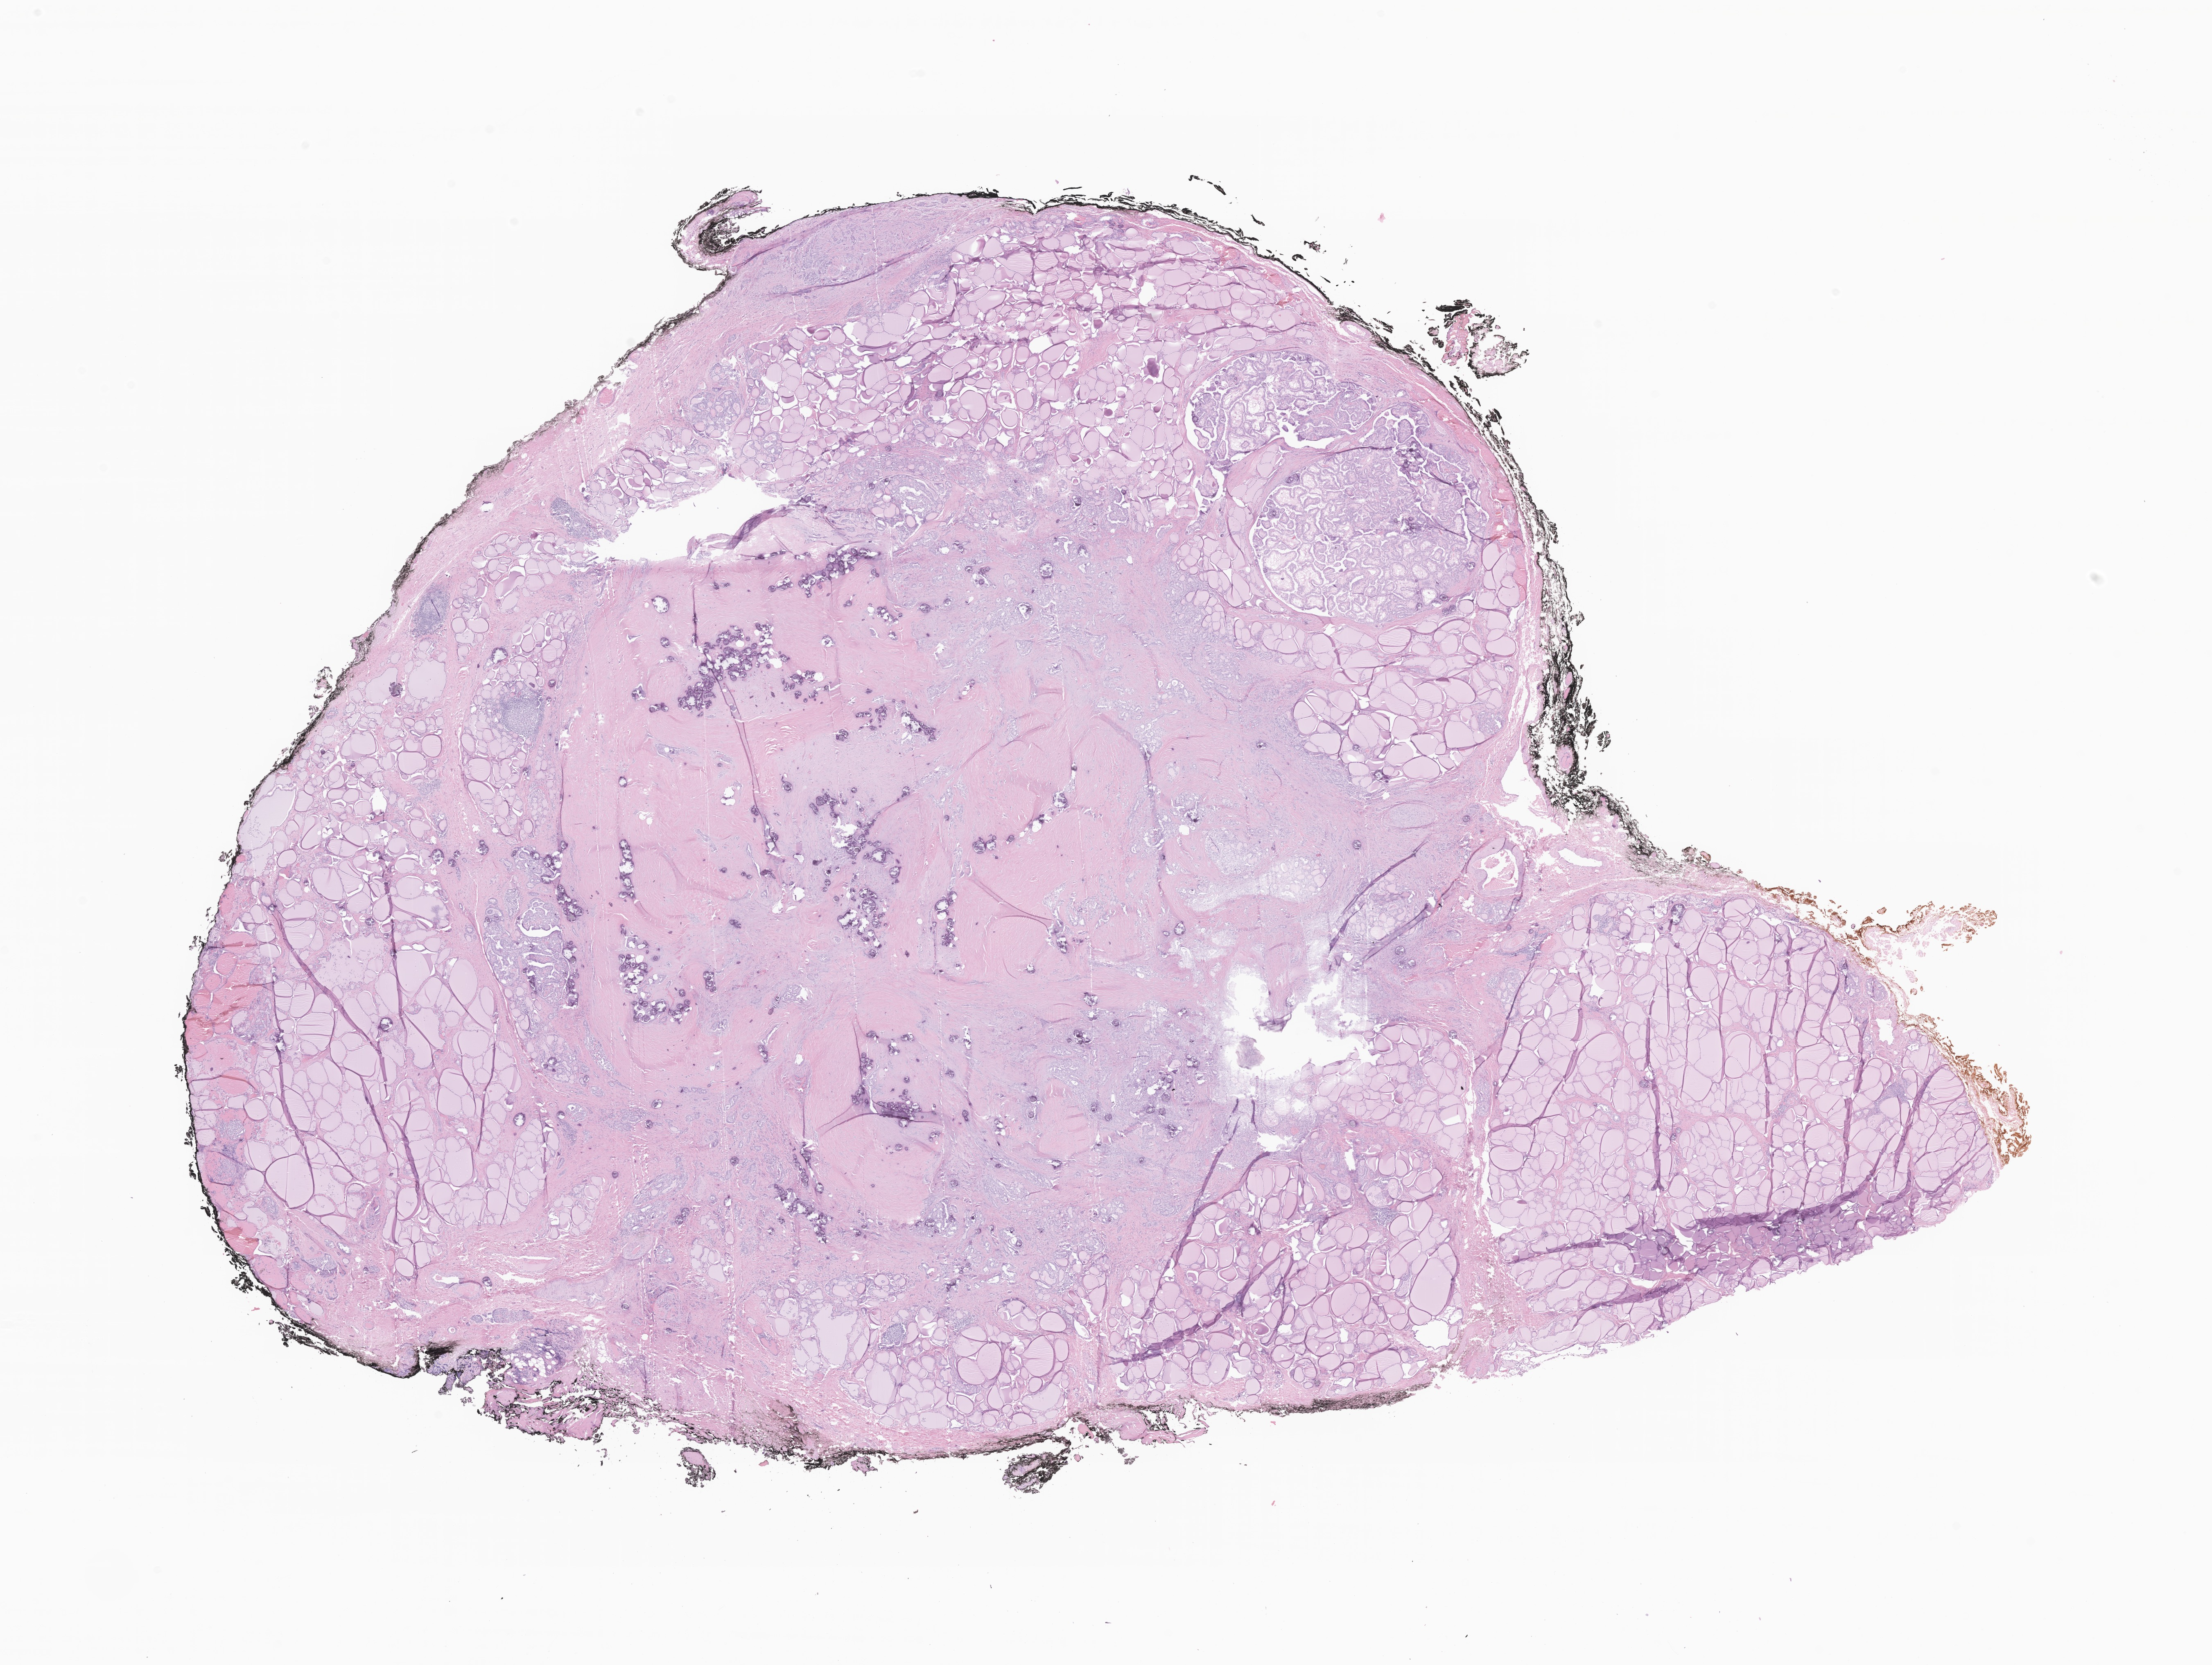
Whole-slide image, hematoxylin and eosin (H&E) stain of tumor tissue from the thyroid — shown as a low-resolution overview of the whole scanned area (about 22.8 x 17.1 mm), FFPE section. Patient female; age 204 months (17 years).
Diagnosis (ICD-O-3 morphology term): Papillary carcinoma, NOS.